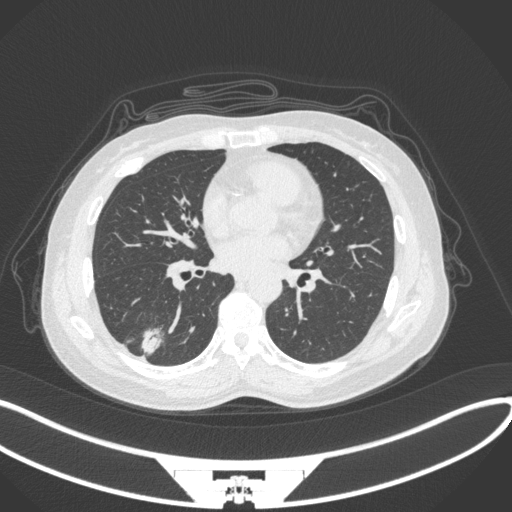
Chest CT, one axial slice. Slice 136 of 352 in the series (ordered by position). Reconstruction kernel B31f. 120 kVp. Lung window (W 1500 / L -600 HU). 512 × 512 image matrix. Female patient, age 55 years. Case-level facts recorded for this patient, not image findings: clinical TNM (as recorded): T1c N1 M0.
Outlined on this slice (bounding box drawn by a radiologist):
- lung tumour (recorded histology: adenocarcinoma): bounding box <135,324,167,357> (left, top, right, bottom; pixels)